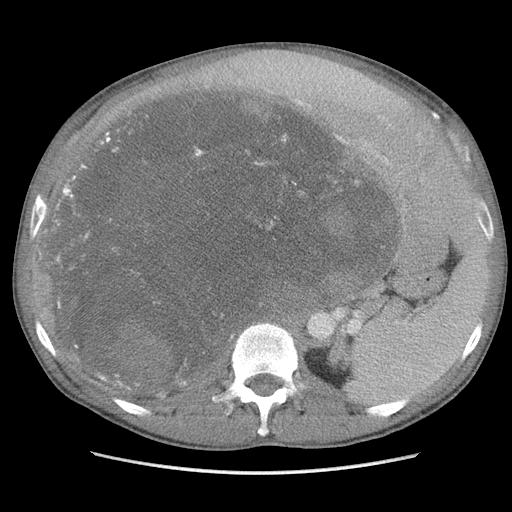
Contrast-enhanced abdominal CT, one axial slice. Position 69 of 115 along the scan axis. Soft-tissue window (W 400 / L 40 HU). 512 × 512 image matrix. Male patient. From the clinical record (not read from this slice): diagnosis: adrenocortical carcinoma; tumour side: right adrenal; Ki-67 index: 13 %; stage (as recorded): 3.
Annotated regions visible in this slice (semi-automatically segmented with operator editing):
- mass: bounding box <54,91,398,387> (left, top, right, bottom; pixels)